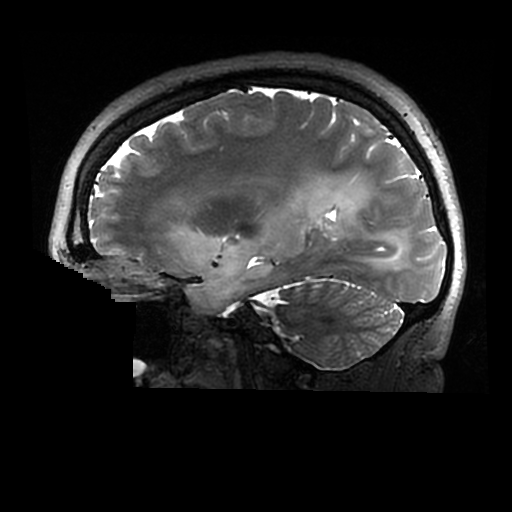
Brain MRI from a brain-tumour surgery series, one sagittal slice. Slice 187 of 320 in the series (ordered by position). 0.6 mm slice thickness. 512 × 512 image matrix, field of view 240 × 240 mm. Case-level facts recorded for this patient, not image findings: histopathology: Astrocytoma; WHO grade: 2; IDH mutation: yes.
Outlined on this slice (manually delineated by an expert):
- tumour: bounding box (x1, y1, x2, y2) in pixels: (173, 180, 407, 310)